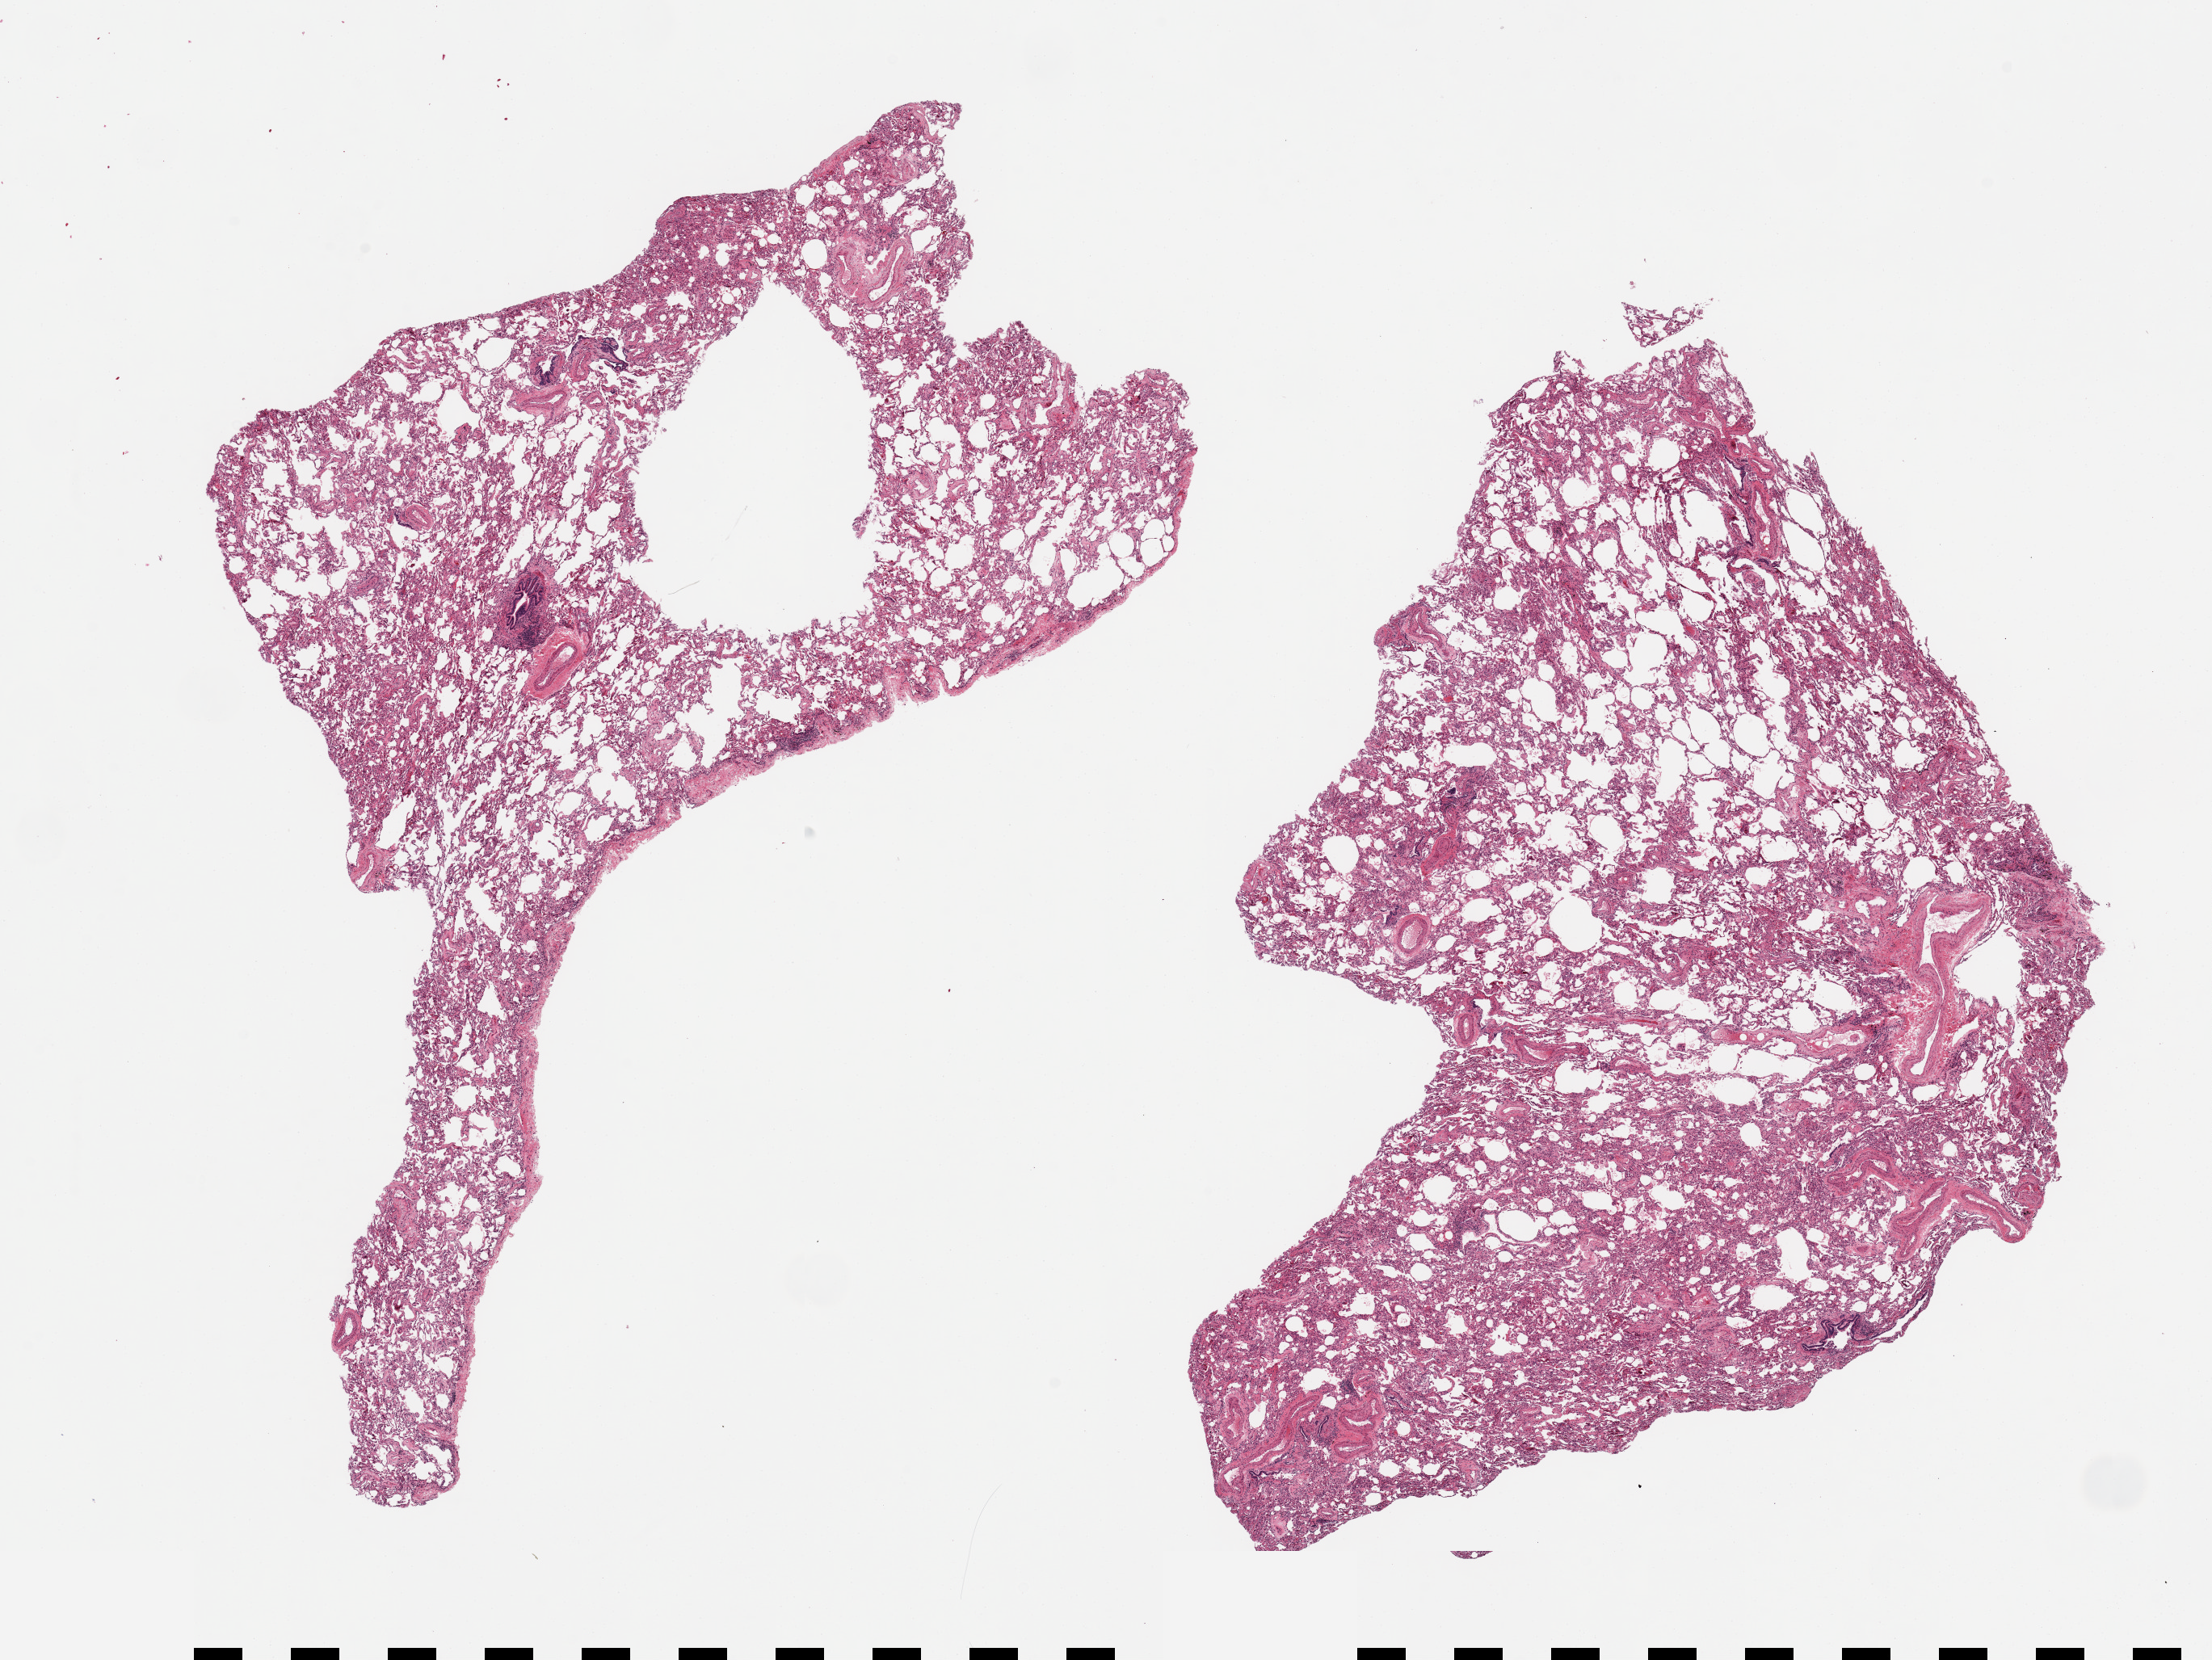
Whole-slide image, hematoxylin and eosin (H&E) stain — a low-resolution overview of the entire scanned area, about 21.7 x 16.3 mm (slide scanned at 20x); PAXgene-fixed, paraffin-embedded tissue; sampled site (target tissue): lung; donor tissue sample.
Review note (as recorded): 2 pieces, focal collections of chronic inflammatory cells and areas of collapse.